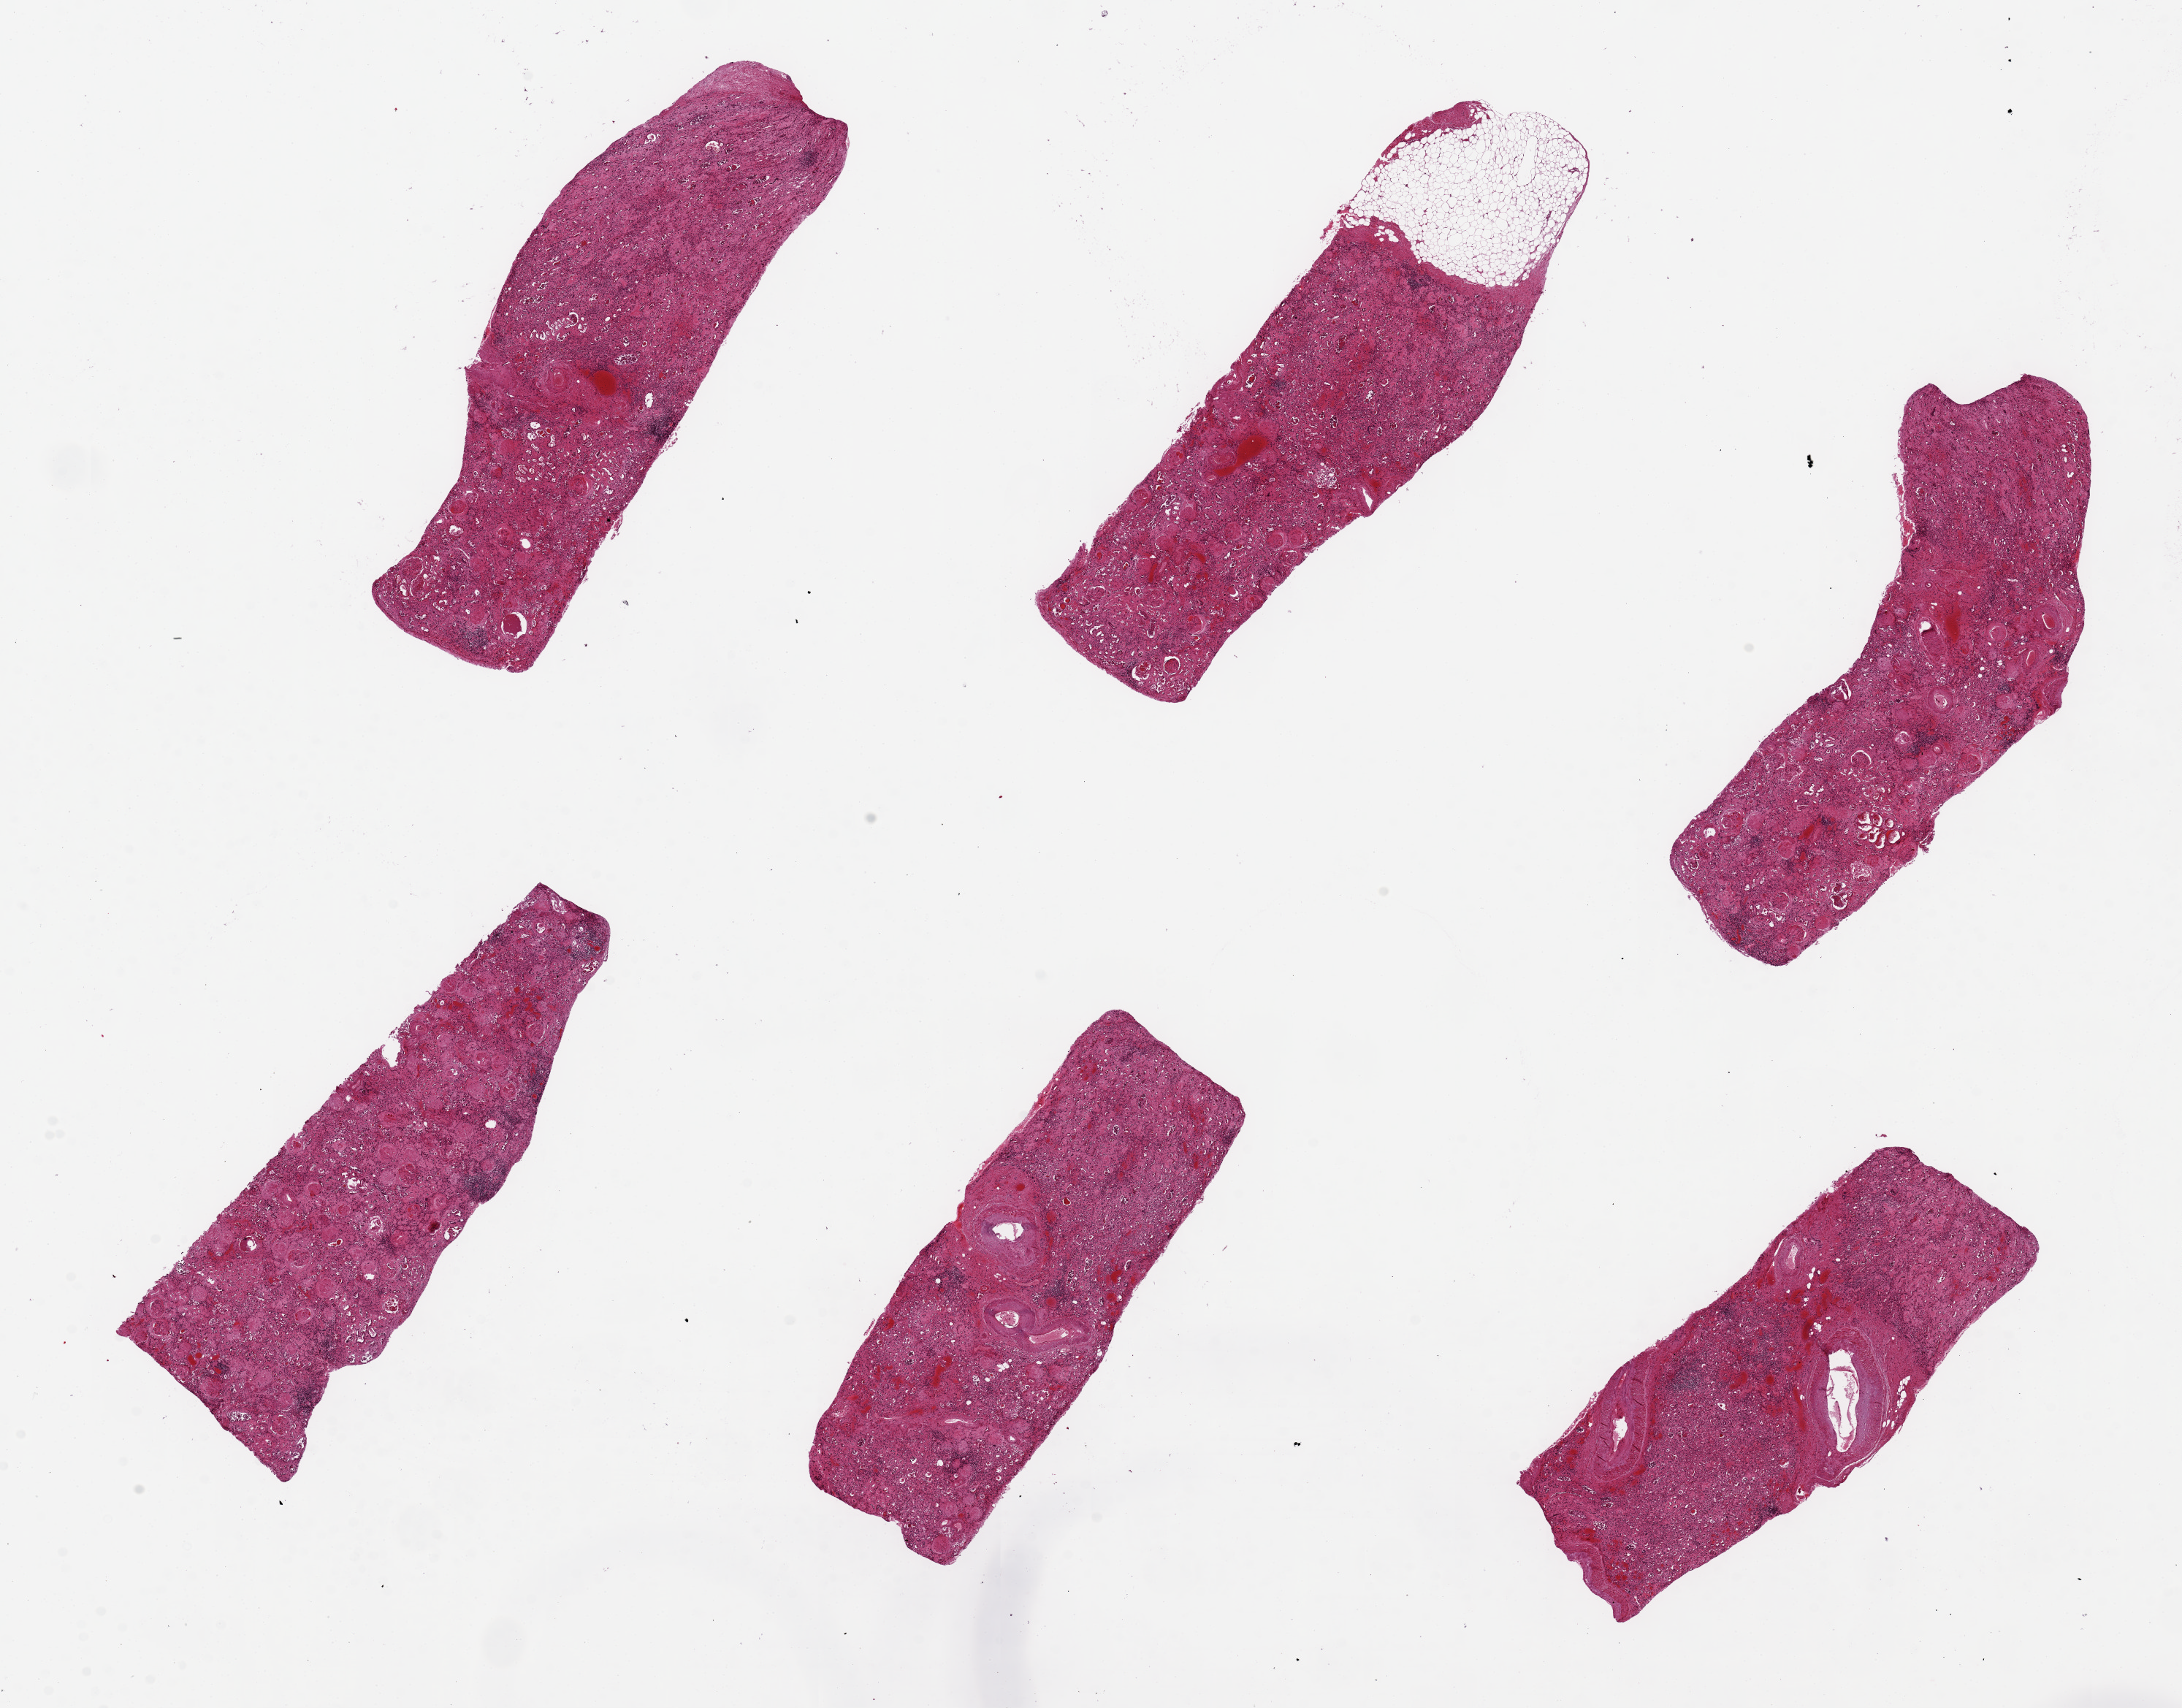
Whole-slide image, haematoxylin and eosin stain — shown as a low-resolution overview of the whole scanned area (about 23.6 x 18.5 mm, from a 20x scan); PAXgene-fixed paraffin-embedded (PFPE) section; section of renal cortex (target tissue); donor tissue sample. Male donor.
• reviewer comment on this tissue sample: 6 pieces, up to 7x2mm; severe glomerulosclerosis consistent with diabetes; no normal glomeruli; mixed cortex and medulla probably due to atrophy of cortex (described grossly)